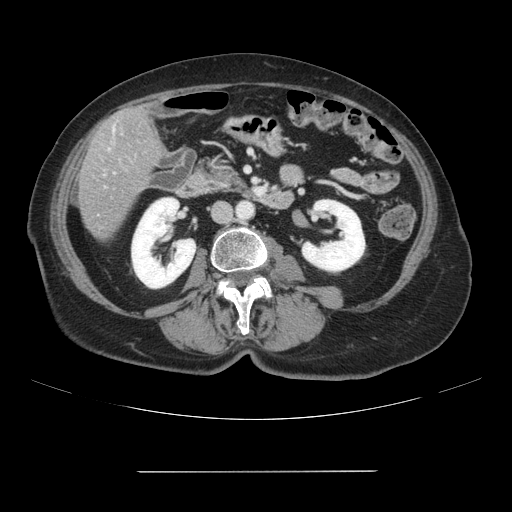
Contrast-enhanced abdominal CT, one axial slice; slice 20 of 111 in the series (ordered by position); intravenous contrast given; soft-tissue window (W 400 / L 40 HU); 2.5 mm slice thickness; 512 × 512 image matrix, field of view 400 × 400 mm. Female patient, age 74 years. From the clinical record (not read from this slice): diagnosis: colorectal cancer liver metastases, imaged before liver resection; multiple liver metastases: yes; largest metastasis: 1.1 cm; disease in both lobes: yes.
Outlined on this slice (outlined manually by an expert reader):
- liver: bounding box [x1, y1, x2, y2] px = [78, 105, 164, 240]